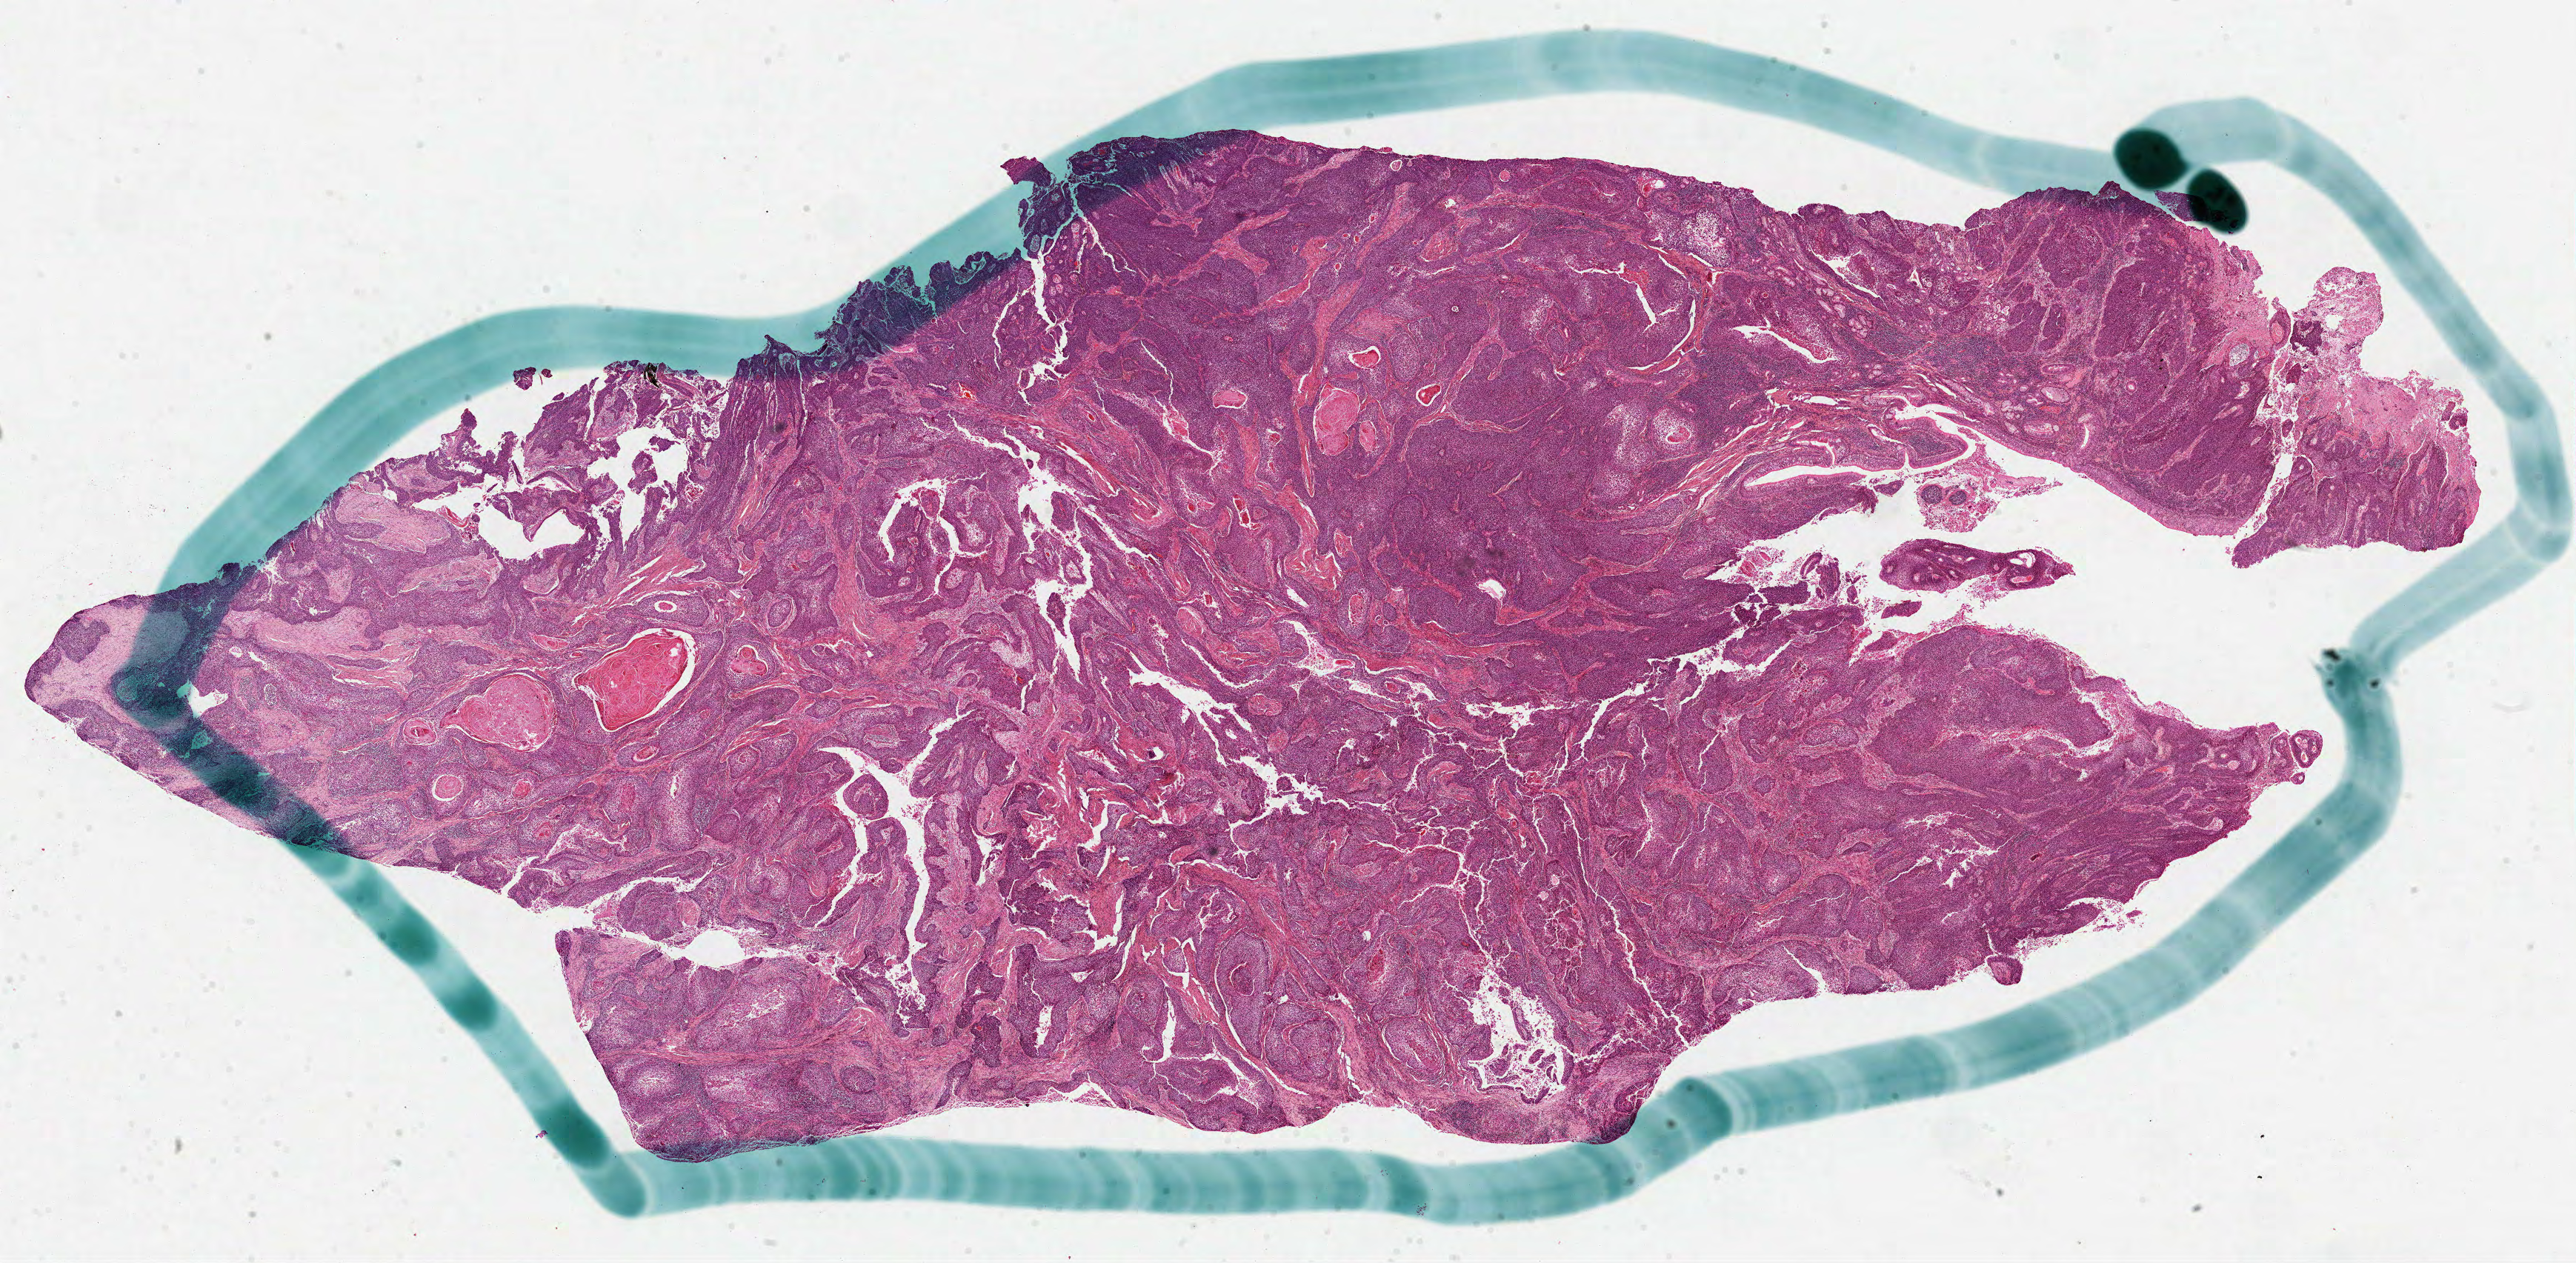
Whole-slide histology image, H&E — shown as a low-resolution overview of the whole scanned area (about 28.0 x 13.8 mm). Formalin-fixed paraffin-embedded (FFPE) diagnostic section. Primary tumour sample from the head and neck. Male, age 58 years at initial diagnosis. Histologic grade: G3 (poorly differentiated).
• AJCC pathologic stage: IVA
• TNM: T4a N0
• pathologic diagnosis: Squamous cell carcinoma, NOS (larynx, NOS)
• lymph nodes positive (case pathology): 0 of 83 examined